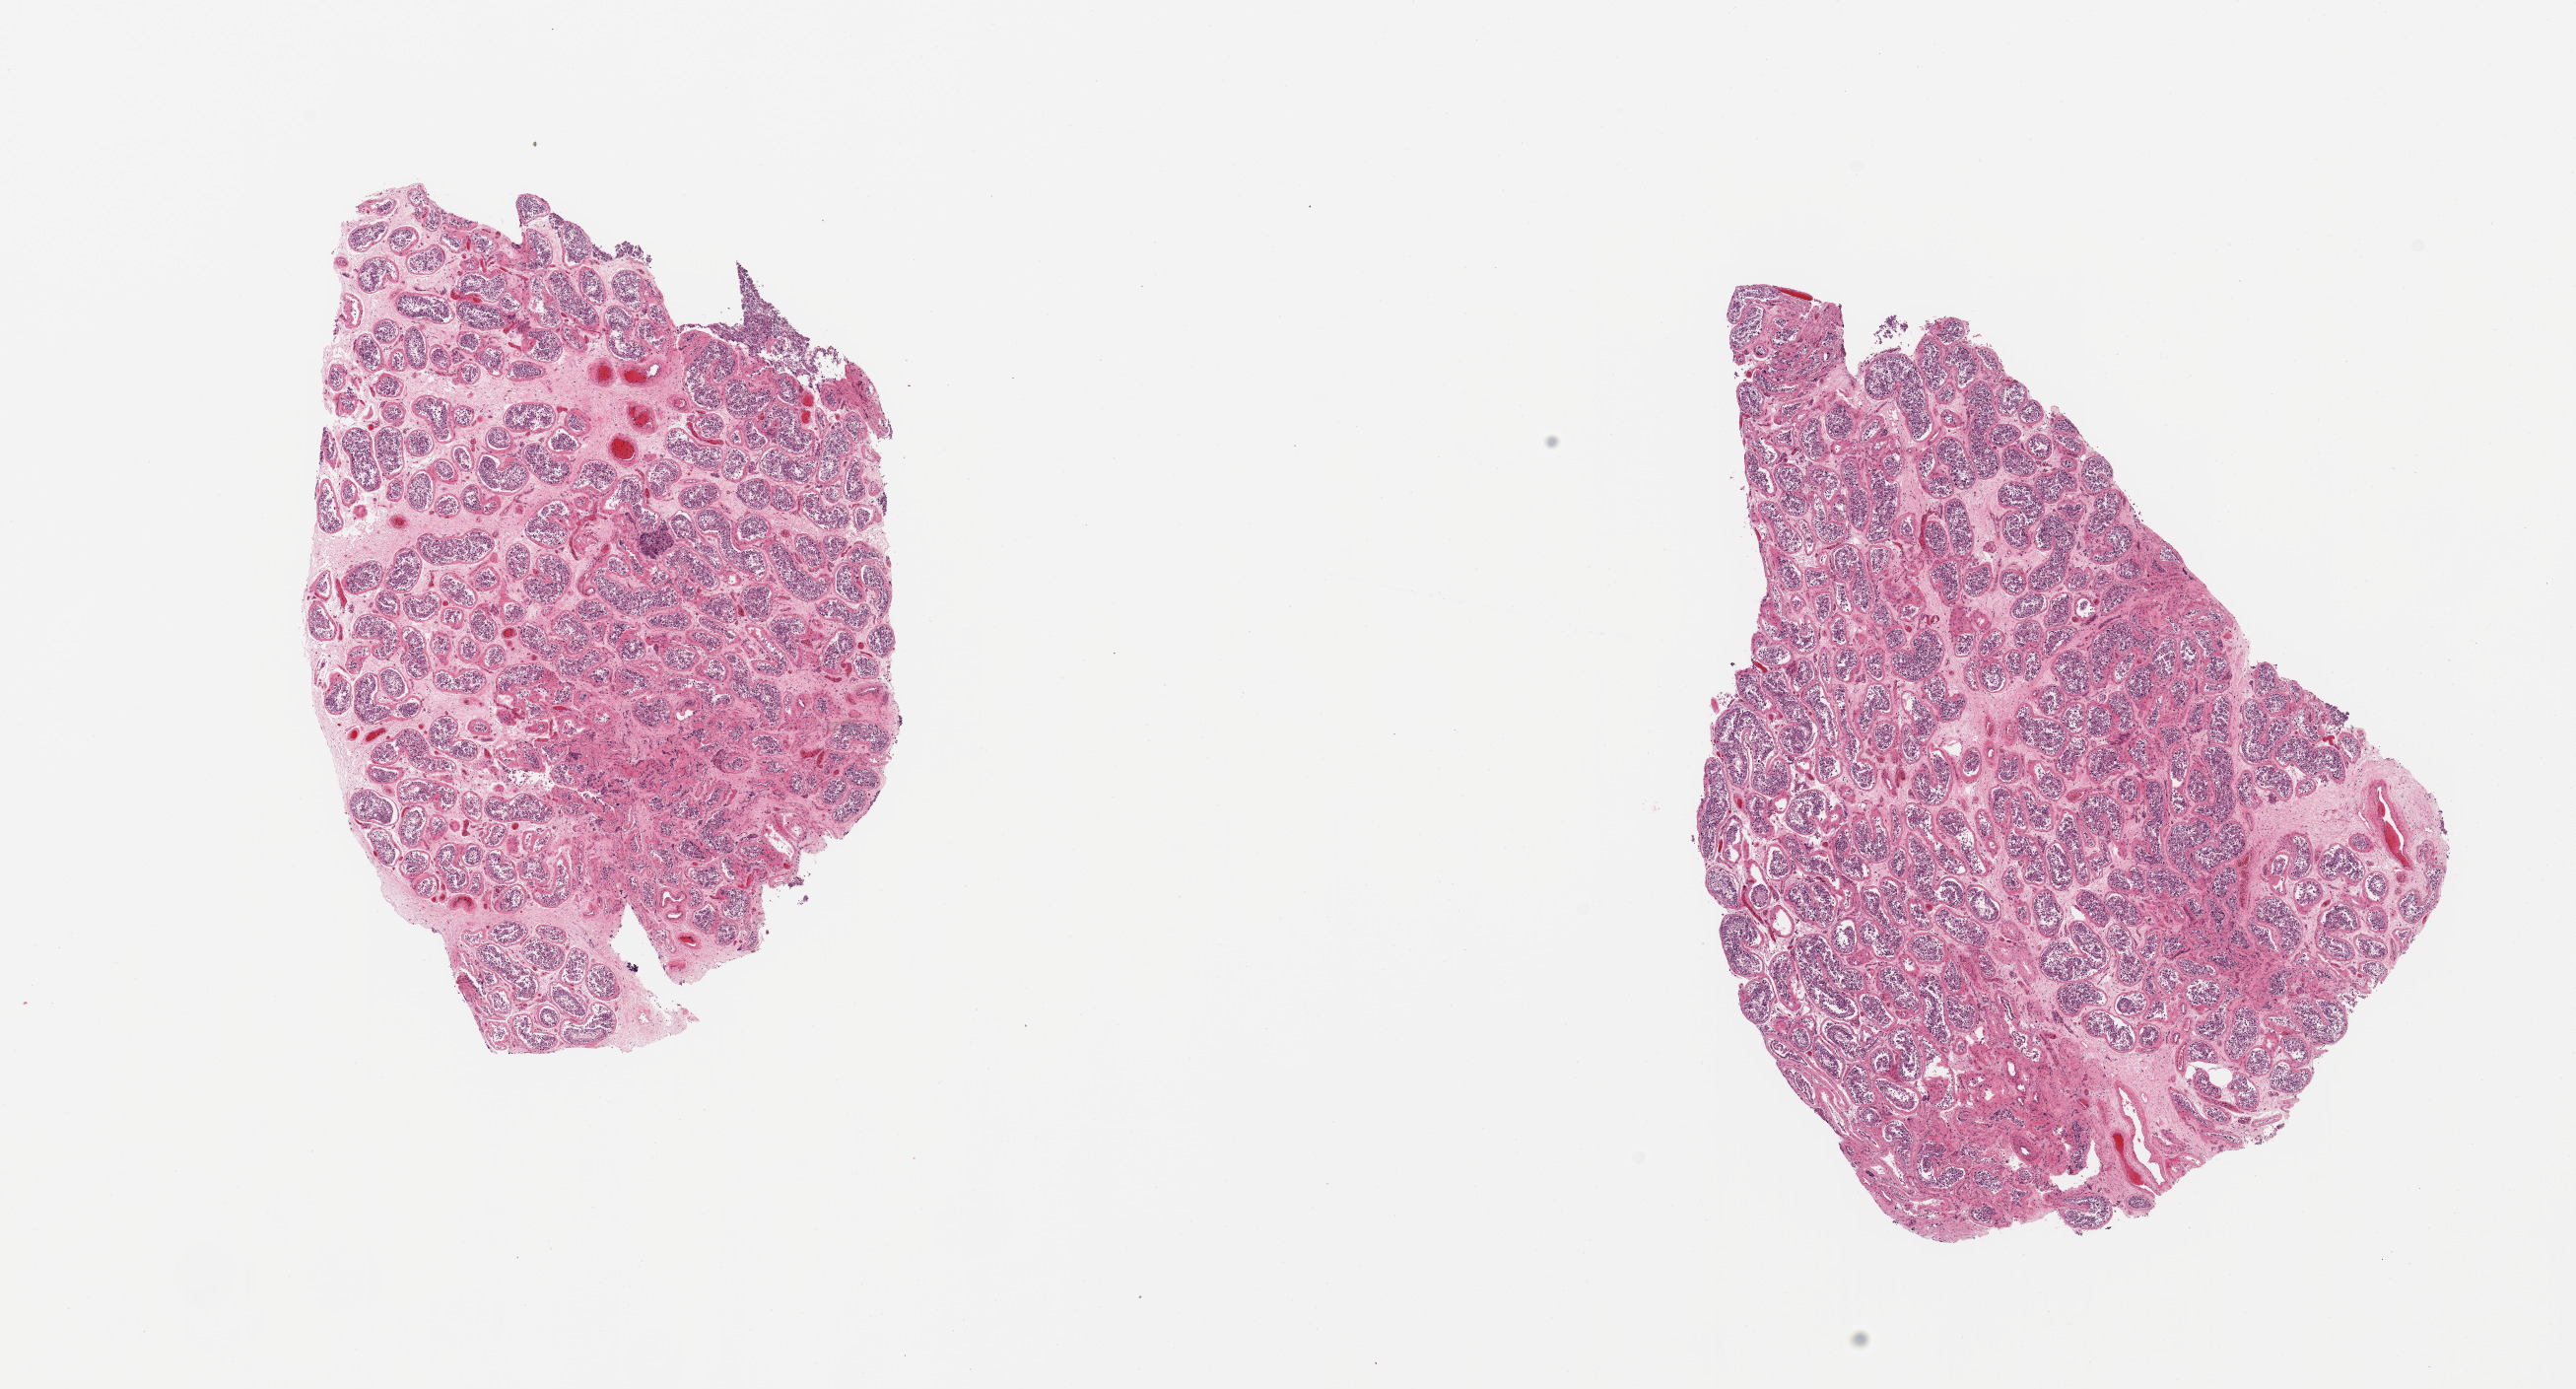
H&E whole-slide image — whole scanned area (about 20.7 x 11.1 mm, slide scanned at 20x) shown as a low-resolution overview. PAXgene-fixed, paraffin-embedded tissue. Sampled site (target tissue): testis. Donor tissue sample. Donor sex: male.
Review note (as recorded): 2 pieces reduced spermatogenesis.